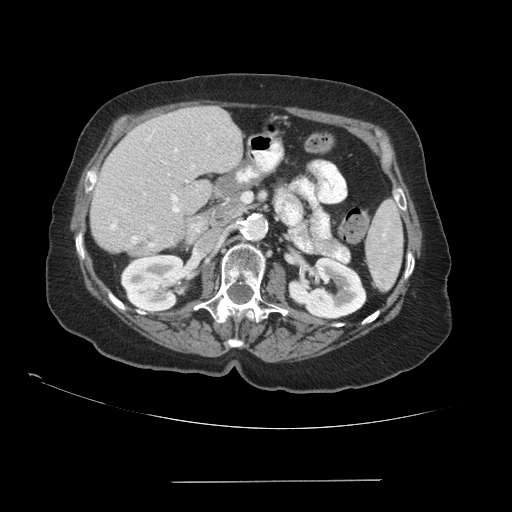
Contrast-enhanced abdominal CT (liver protocol), one axial slice; slice 43 of 89 in the series (ordered by position); reconstruction kernel STANDARD; soft-tissue window (W 400 / L 40 HU); 2.5 mm slice thickness; 512 × 512 image matrix, field of view 400 × 400 mm. From the clinical record (not read from this slice): diagnosis: hepatocellular carcinoma (patient treated with transarterial chemoembolisation; whether this scan precedes or follows treatment is not stated here); TNM stage (as recorded): Stage-IVA; Child-Pugh class: A; tumour nodularity: uninodular.
Annotated regions visible in this slice (semi-automatic segmentation, software-assisted and operator-edited):
- liver parenchyma outside the tumour (the mass and vessels are separate outlines, so this box may not span the whole liver): box from (x=90, y=106) to (x=242, y=252) px
- liver vessels: (x=110, y=136)–(x=188, y=243)